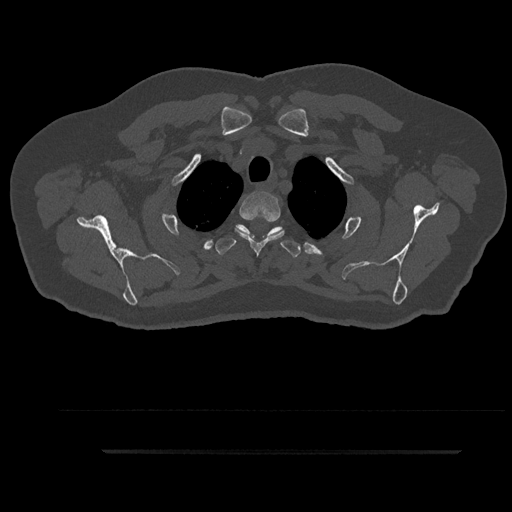
CT including the spine, one axial slice; position 744 of 797 along the scan axis; reconstruction kernel Br40s/3; bone window (W 1800 / L 400 HU); 0.5 mm slice thickness; 512 × 512 image matrix, field of view 432 × 432 mm. Male patient, age 63 years. Case-level facts recorded for this patient, not image findings: primary cancer: renal; vertebrae with lytic lesions (as recorded): T8.
Structures marked on this image (semi-automatic segmentation, software-assisted and operator-edited):
- T2 vertebra: bounding box <235,191,284,255> (left, top, right, bottom; pixels)
- T3 vertebra: <215,224,302,258>